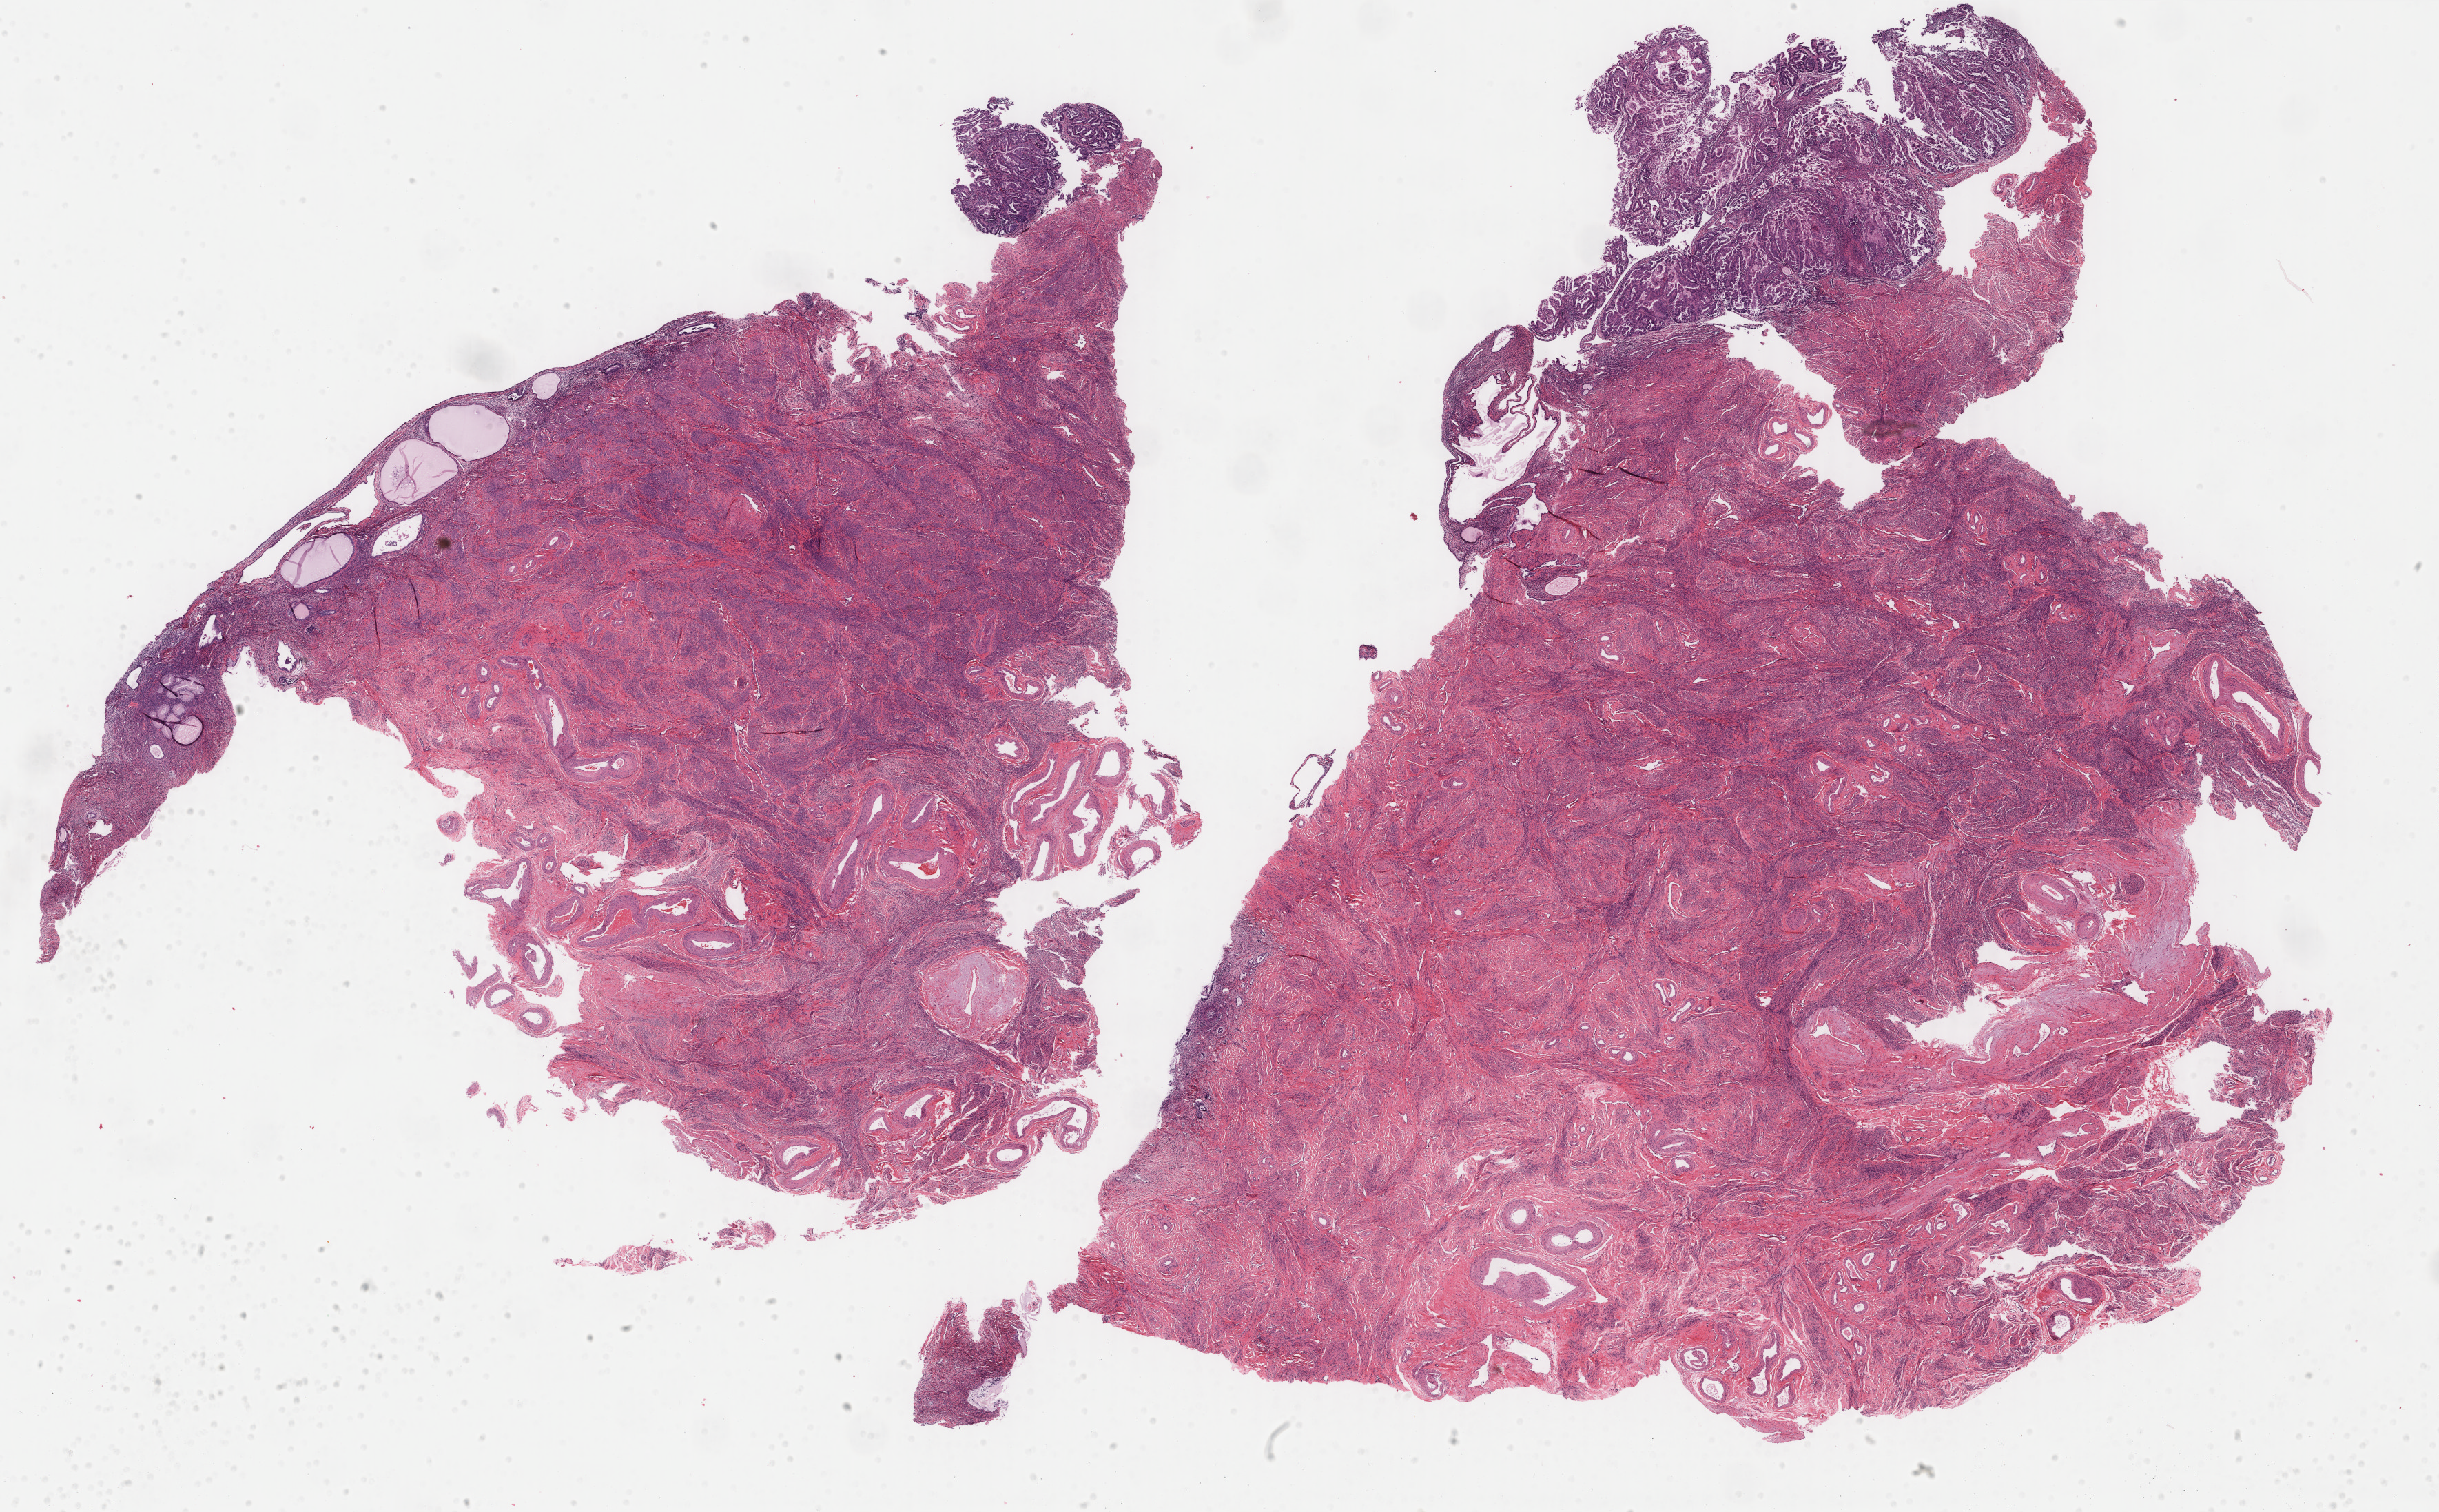
Whole-slide histology image, Hematoxylin and eosin (H&E) stained, shown as a low-resolution overview of the whole scanned area (about 28.1 x 17.4 mm). Formalin-fixed paraffin-embedded (FFPE) diagnostic section. Uterus, primary tumour sample. Female, age 60 years at initial diagnosis. Histologic grade: G2 (moderately differentiated).
FIGO stage: IB. Histologic diagnosis: Endometrioid adenocarcinoma, NOS (endometrium).